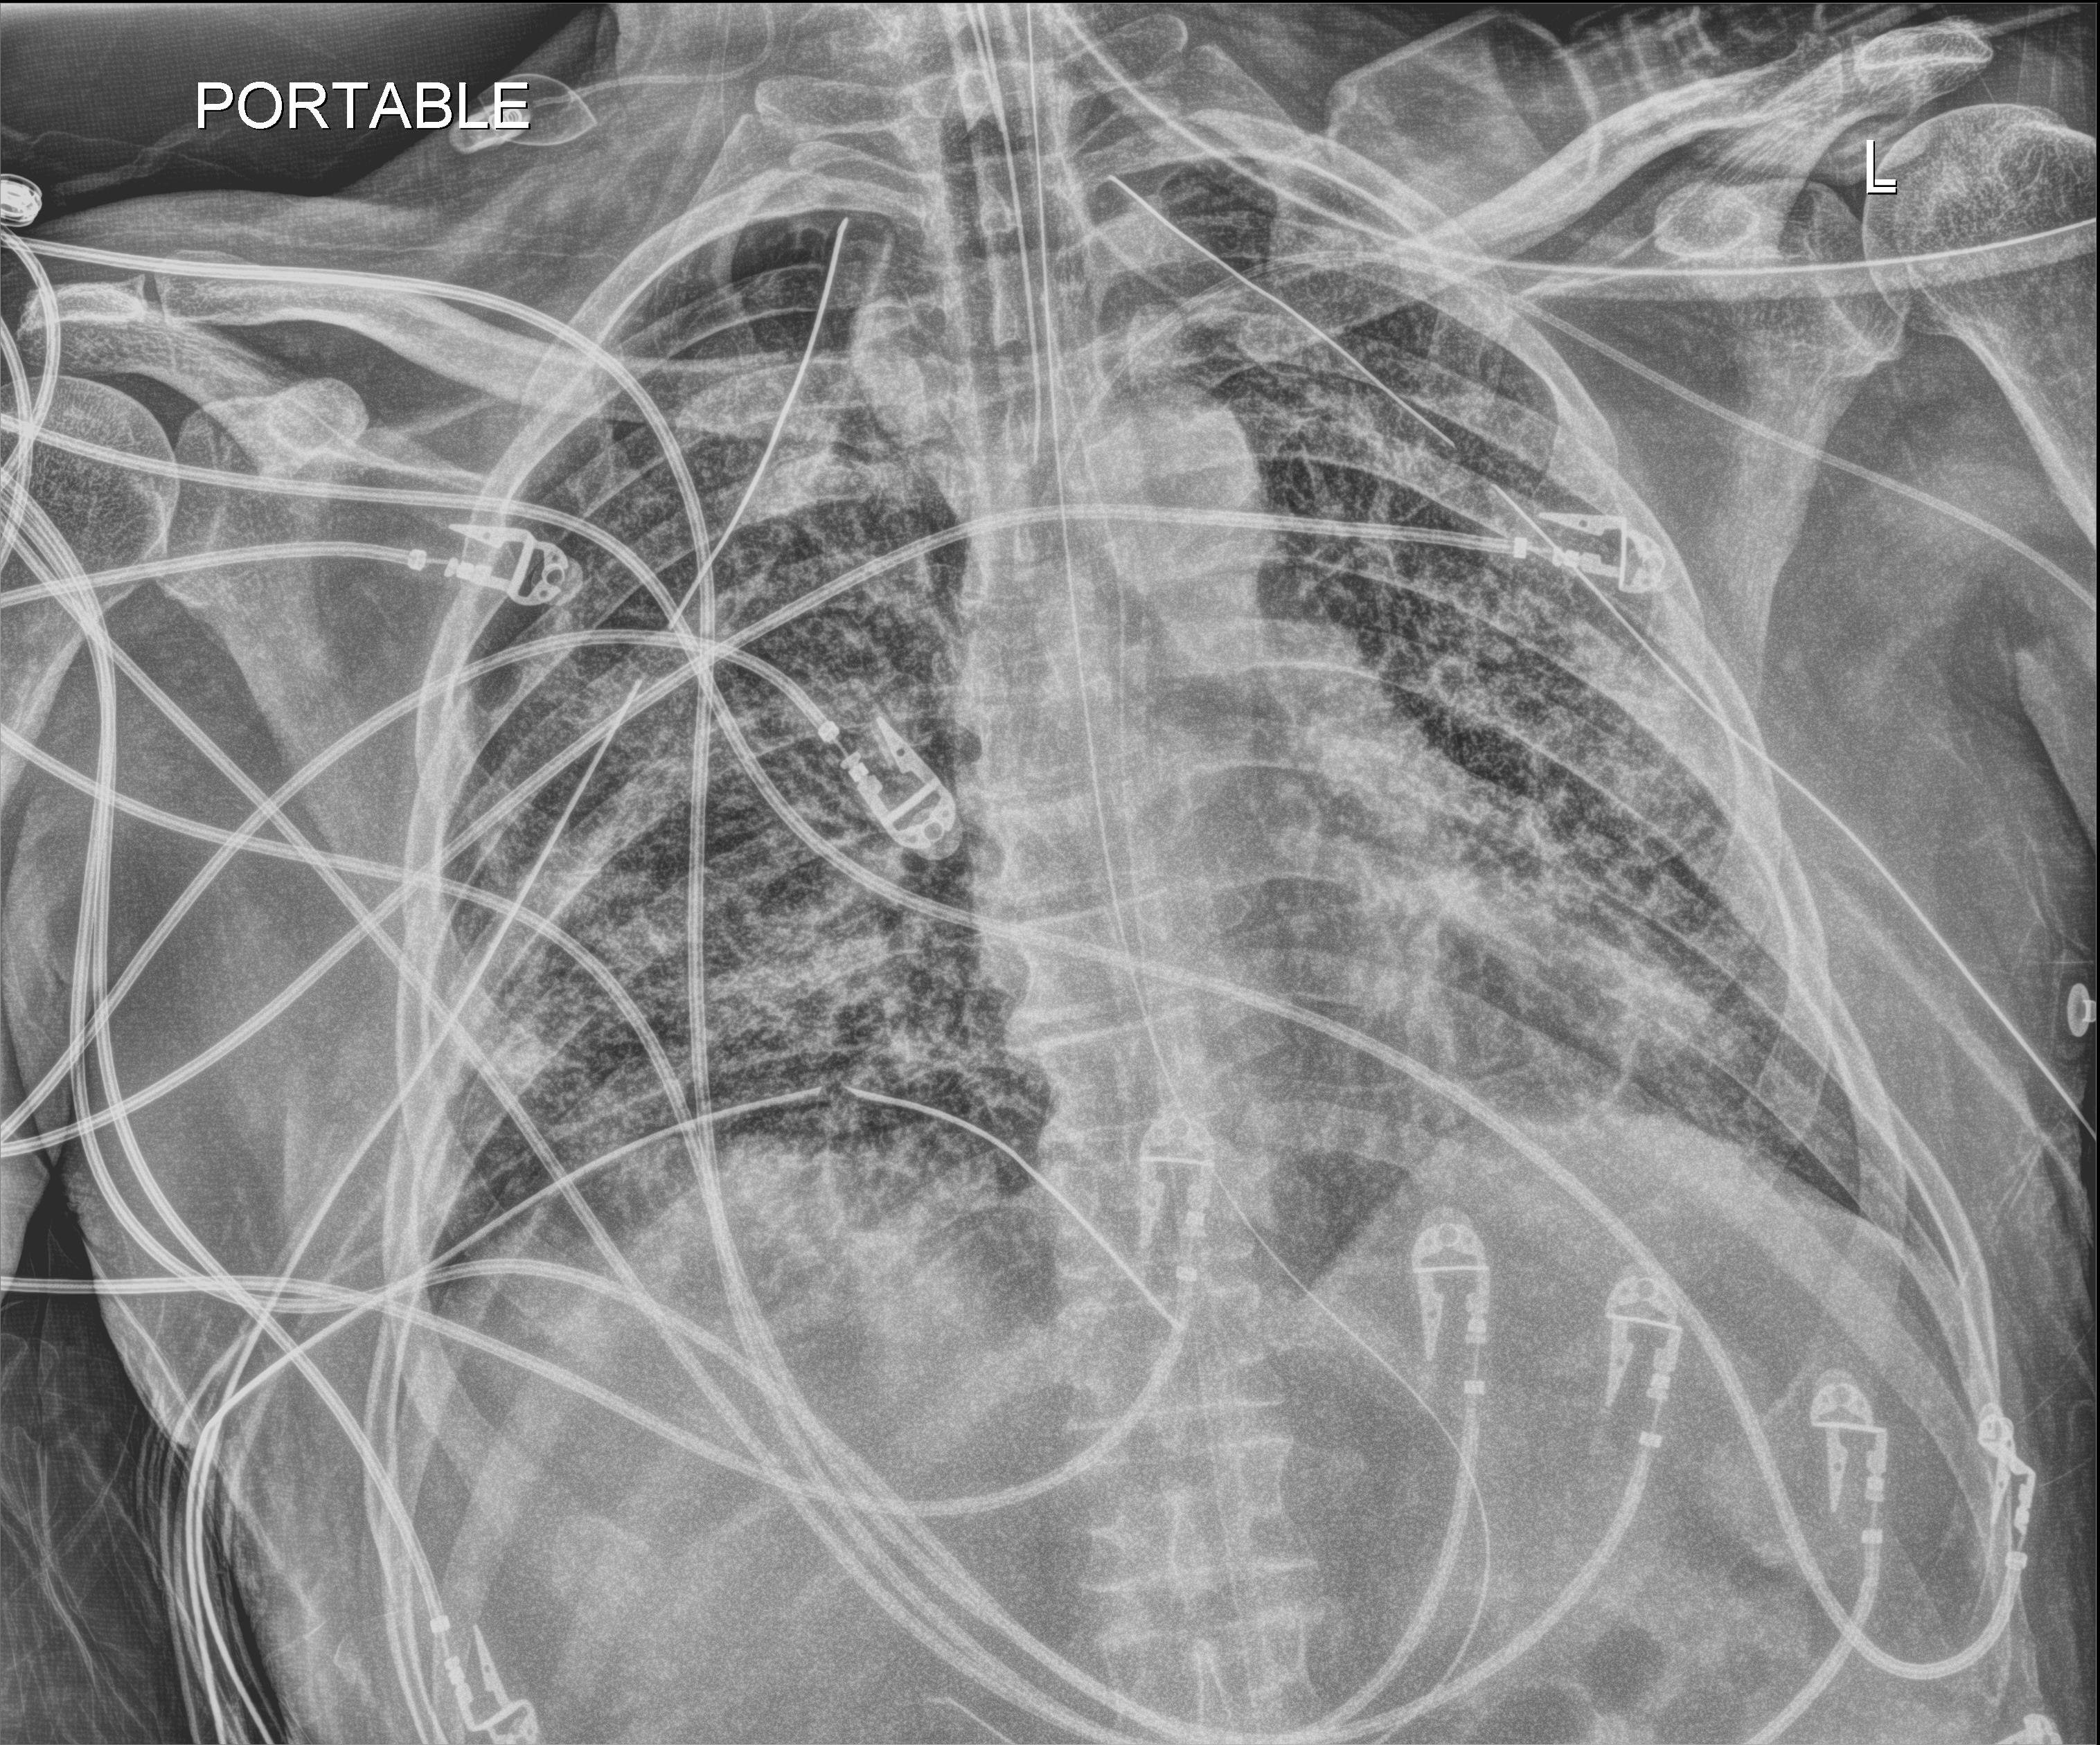
Portable chest radiograph, anteroposterior (AP) projection. Patient hospitalised with COVID-19; male, aged 18–59 years.
Hospital-stay facts (about this admission, not read from this image; timing relative to this image not recorded): other chronic lung disease (admission record): no; admitted to intensive care during this hospital stay: yes; diabetes (admission record): no.